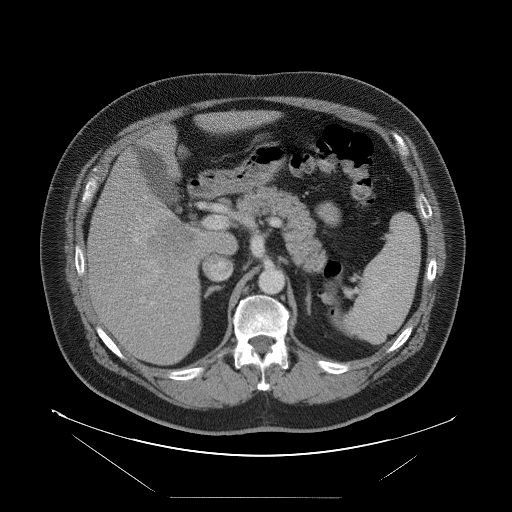
Contrast-enhanced abdominal CT, one axial slice; slice 55 of 114 in the series (ordered by position); 120 kVp; soft-tissue window (W 400 / L 40 HU); 512 × 512 image matrix, field of view 500 × 500 mm. Male patient, age 61 years. Case-level facts recorded for this patient, not image findings: diagnosis: colorectal cancer liver metastases, imaged before liver resection; multiple liver metastases: no; largest metastasis: 6.5 cm; disease in both lobes: yes.
Structures marked on this image (outlined manually by an expert reader):
- liver: box from (x=89, y=111) to (x=269, y=365) px
- planned liver remnant (the part of the liver to remain after resection): (x=145, y=112)–(x=269, y=174)
- liver metastasis: (x=149, y=219)–(x=198, y=261)